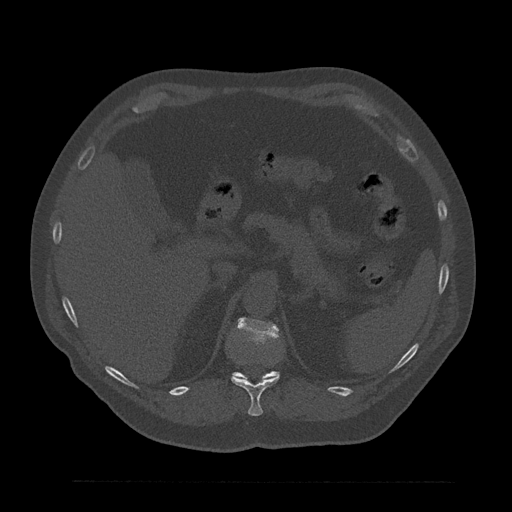
CT including the spine, one axial slice. Slice 268 of 797 in the series (ordered by position). Reconstruction kernel Br40s/3. 120 kVp. Bone window (W 1800 / L 400 HU). 0.5 mm slice thickness. 512 × 512 image matrix, field of view 430 × 430 mm. Male patient, age 61 years. From the clinical record (not read from this slice): primary cancer: prostate.
Outlined on this slice (semi-automatic segmentation, software-assisted and operator-edited):
- L1 vertebra: bounding box <244,378,267,380> (left, top, right, bottom; pixels)
- T11 vertebra: <231,376,279,416>
- T12 vertebra: <233,318,279,380>